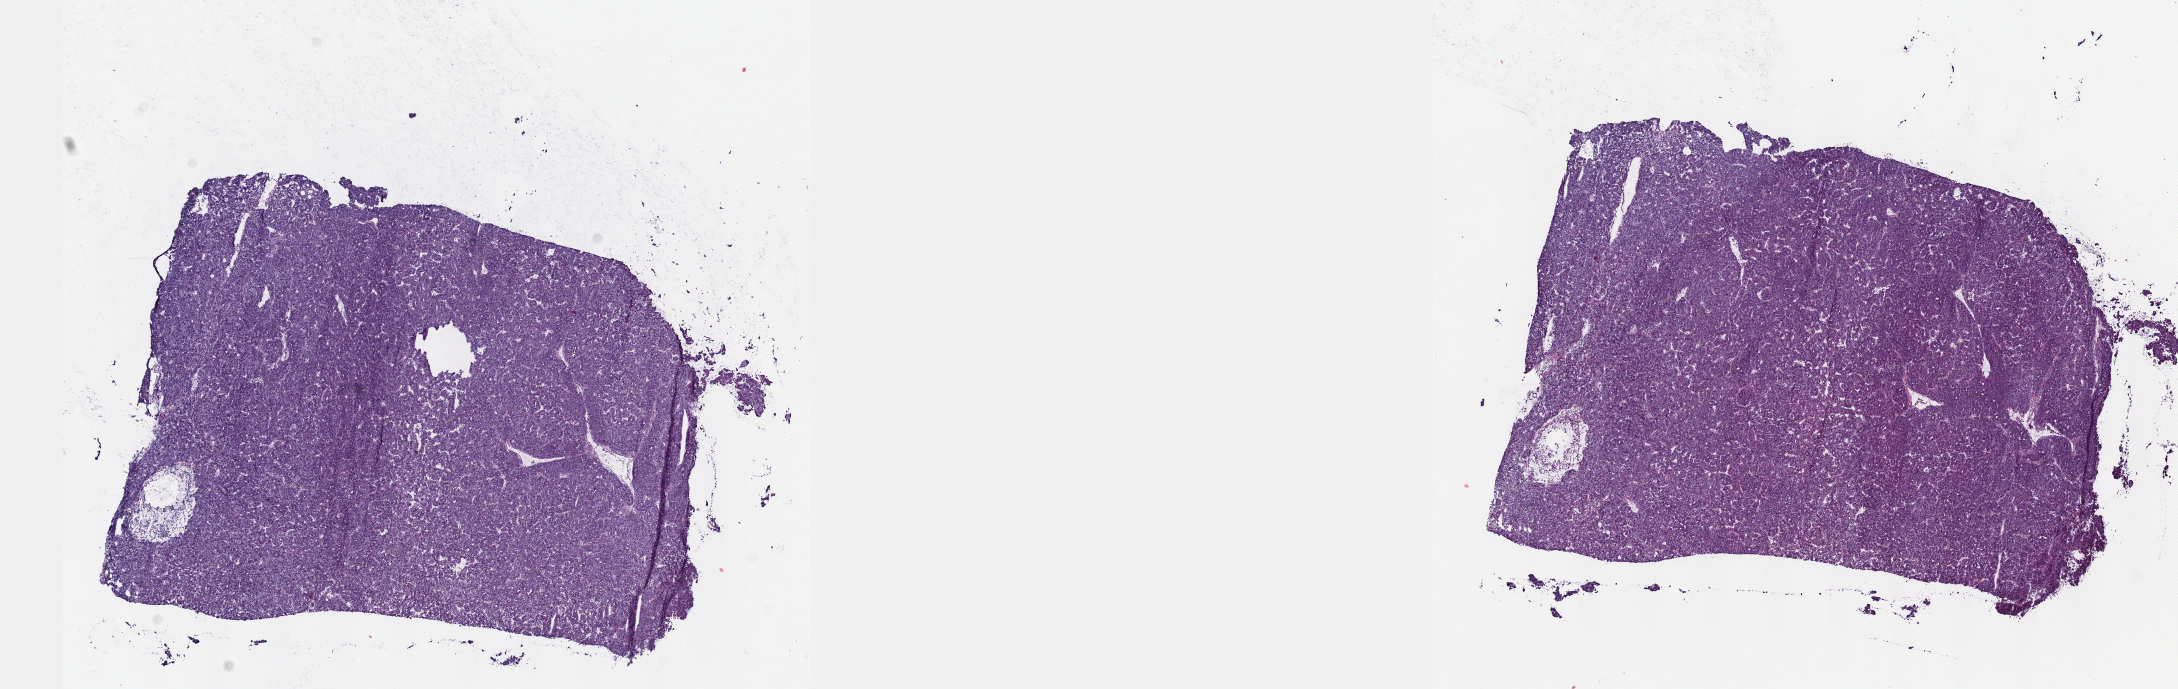
H&E-stained whole-slide image, low-resolution overview of the scanned area, about 17.6 x 5.6 mm (slide scanned at 40x), frozen section, sample: primary tumour, liver. Patient: male, age at initial diagnosis 58 years. Histologic grade: G2 (moderately differentiated). Slide review estimates, as recorded: tumour cells 85%, tumour nuclei 85%, normal cells 0%, stromal cells 15%, necrosis 0%. Inflammatory infiltration, as recorded: lymphocyte infiltration 3%, monocyte infiltration 1%, neutrophil infiltration 1%.
- histologic diagnosis: Hepatocellular carcinoma, NOS
- AJCC pathologic stage: I (7th edition)